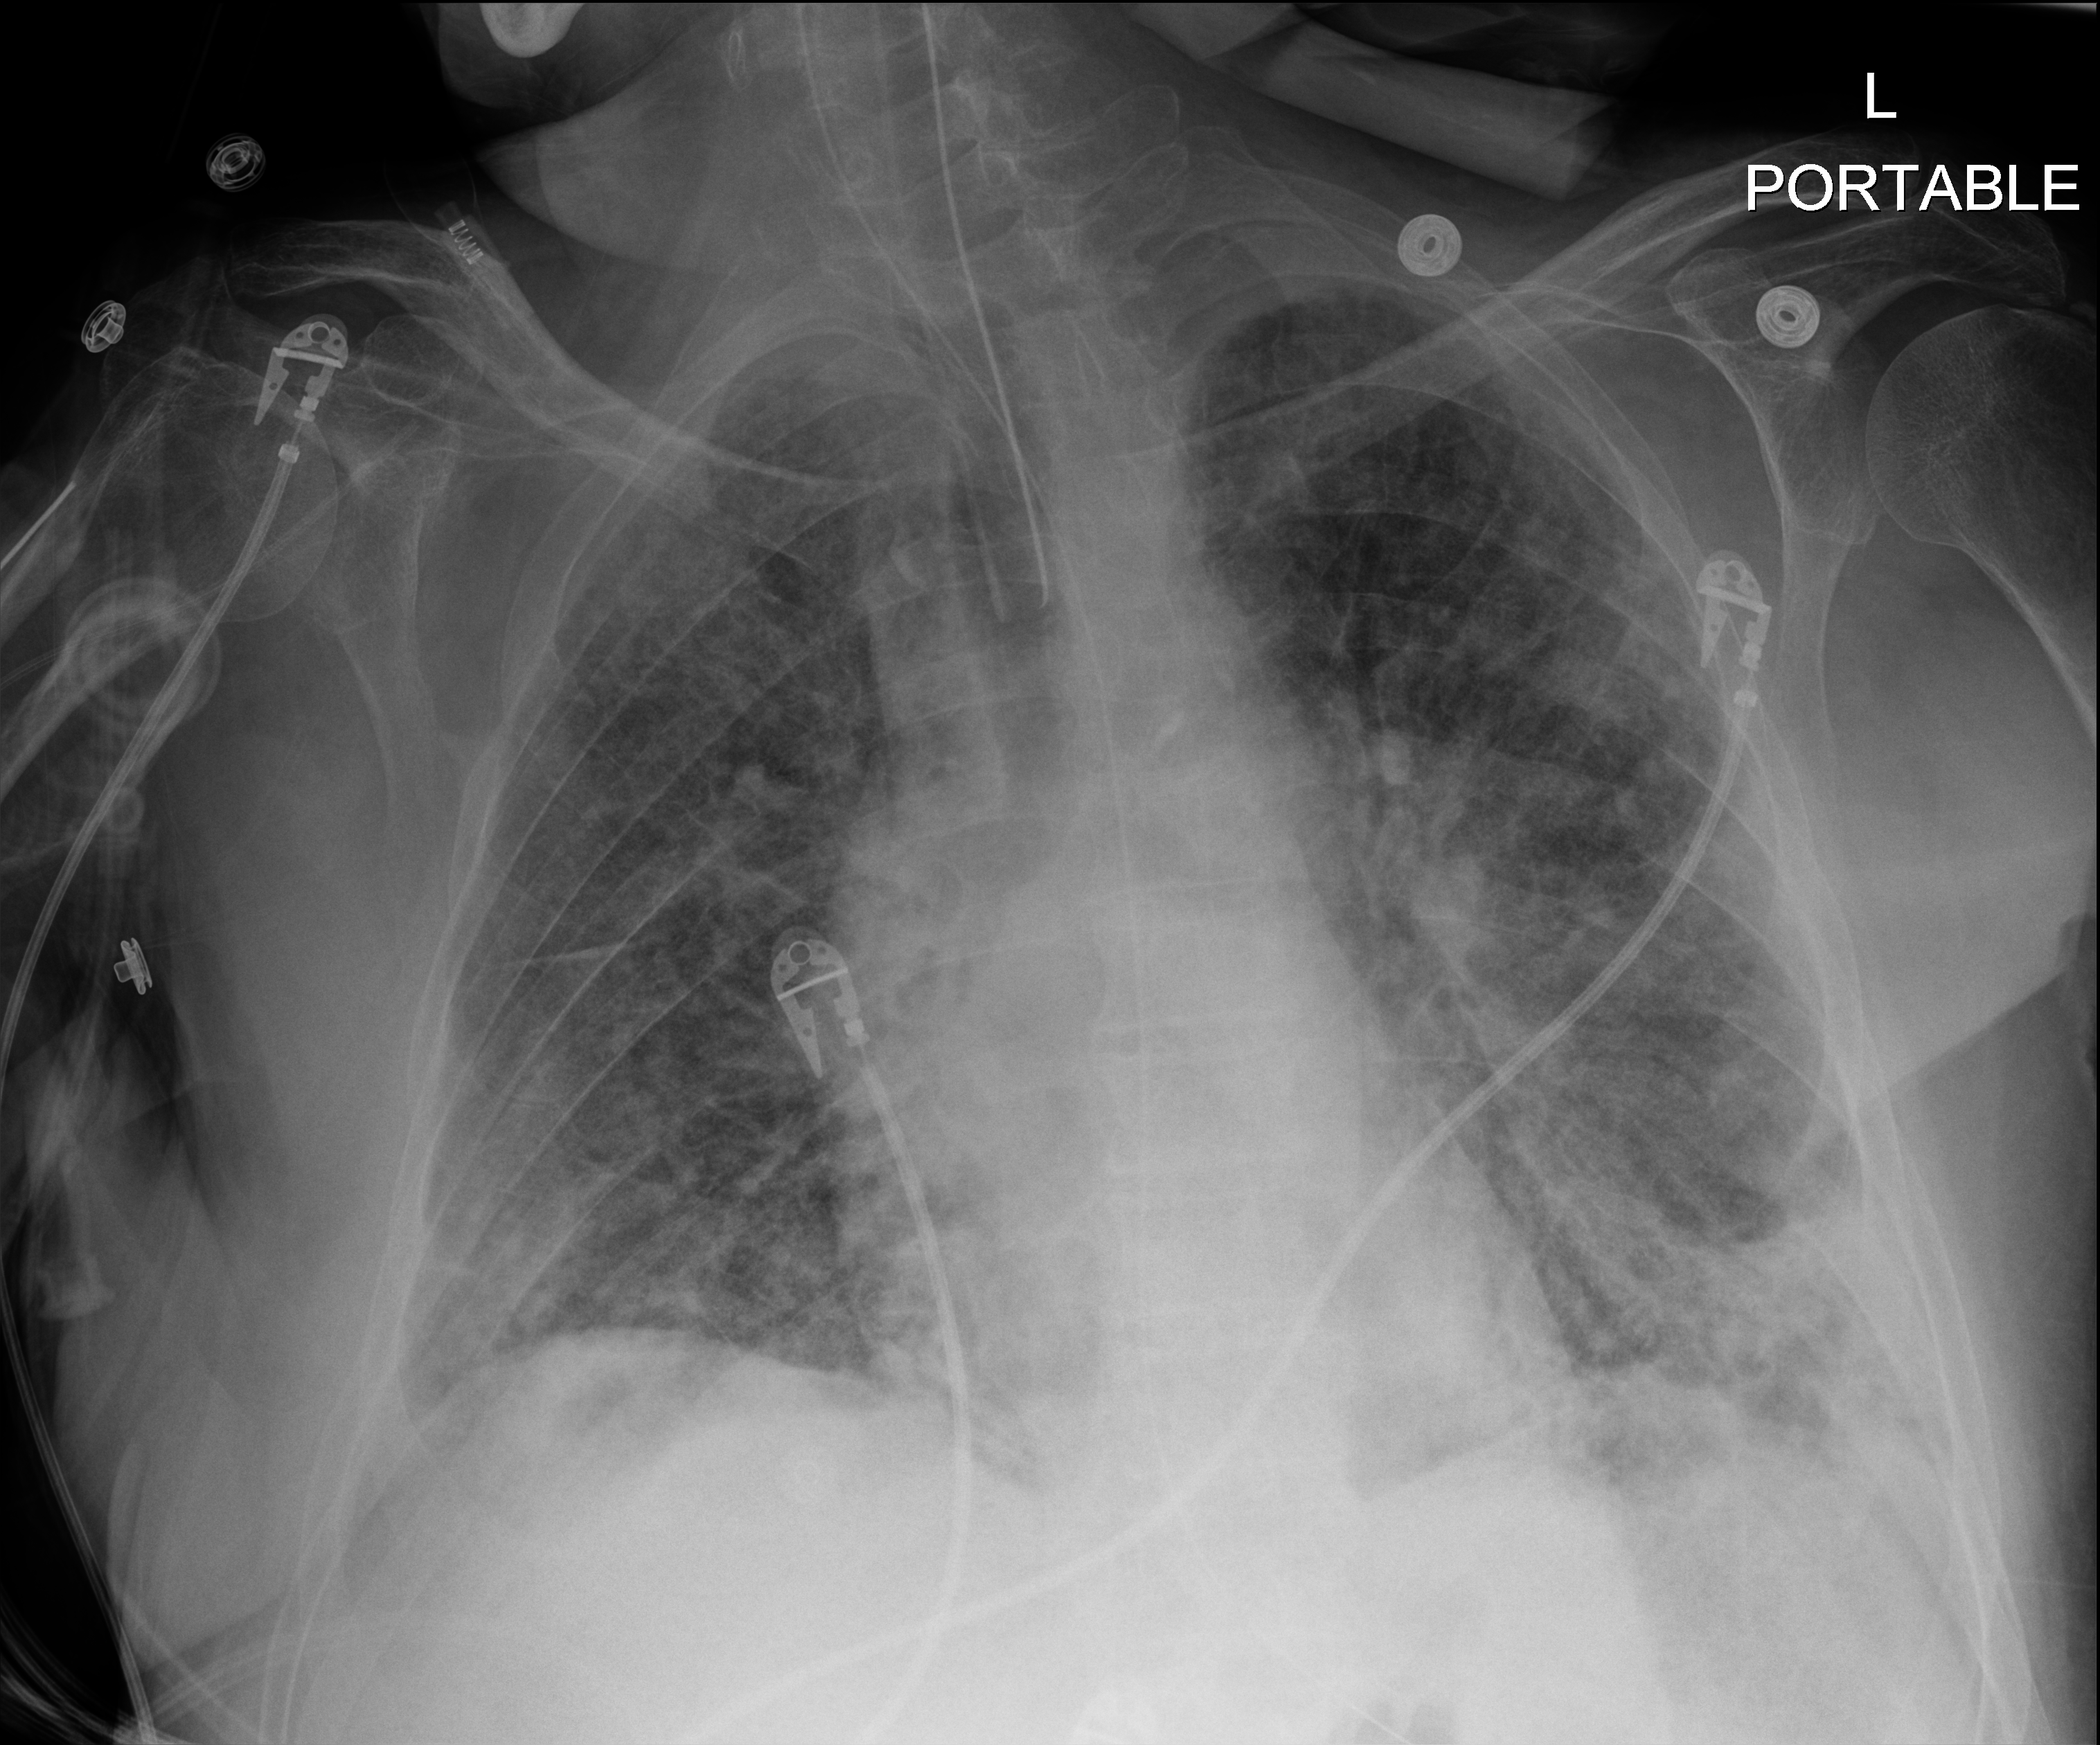
Chest X-ray, anteroposterior (AP) projection. Patient hospitalised with COVID-19; male, aged 60–74 years.
Admission-level facts for this patient (not findings on this image; timing relative to this image not recorded): COPD (admission record): no.